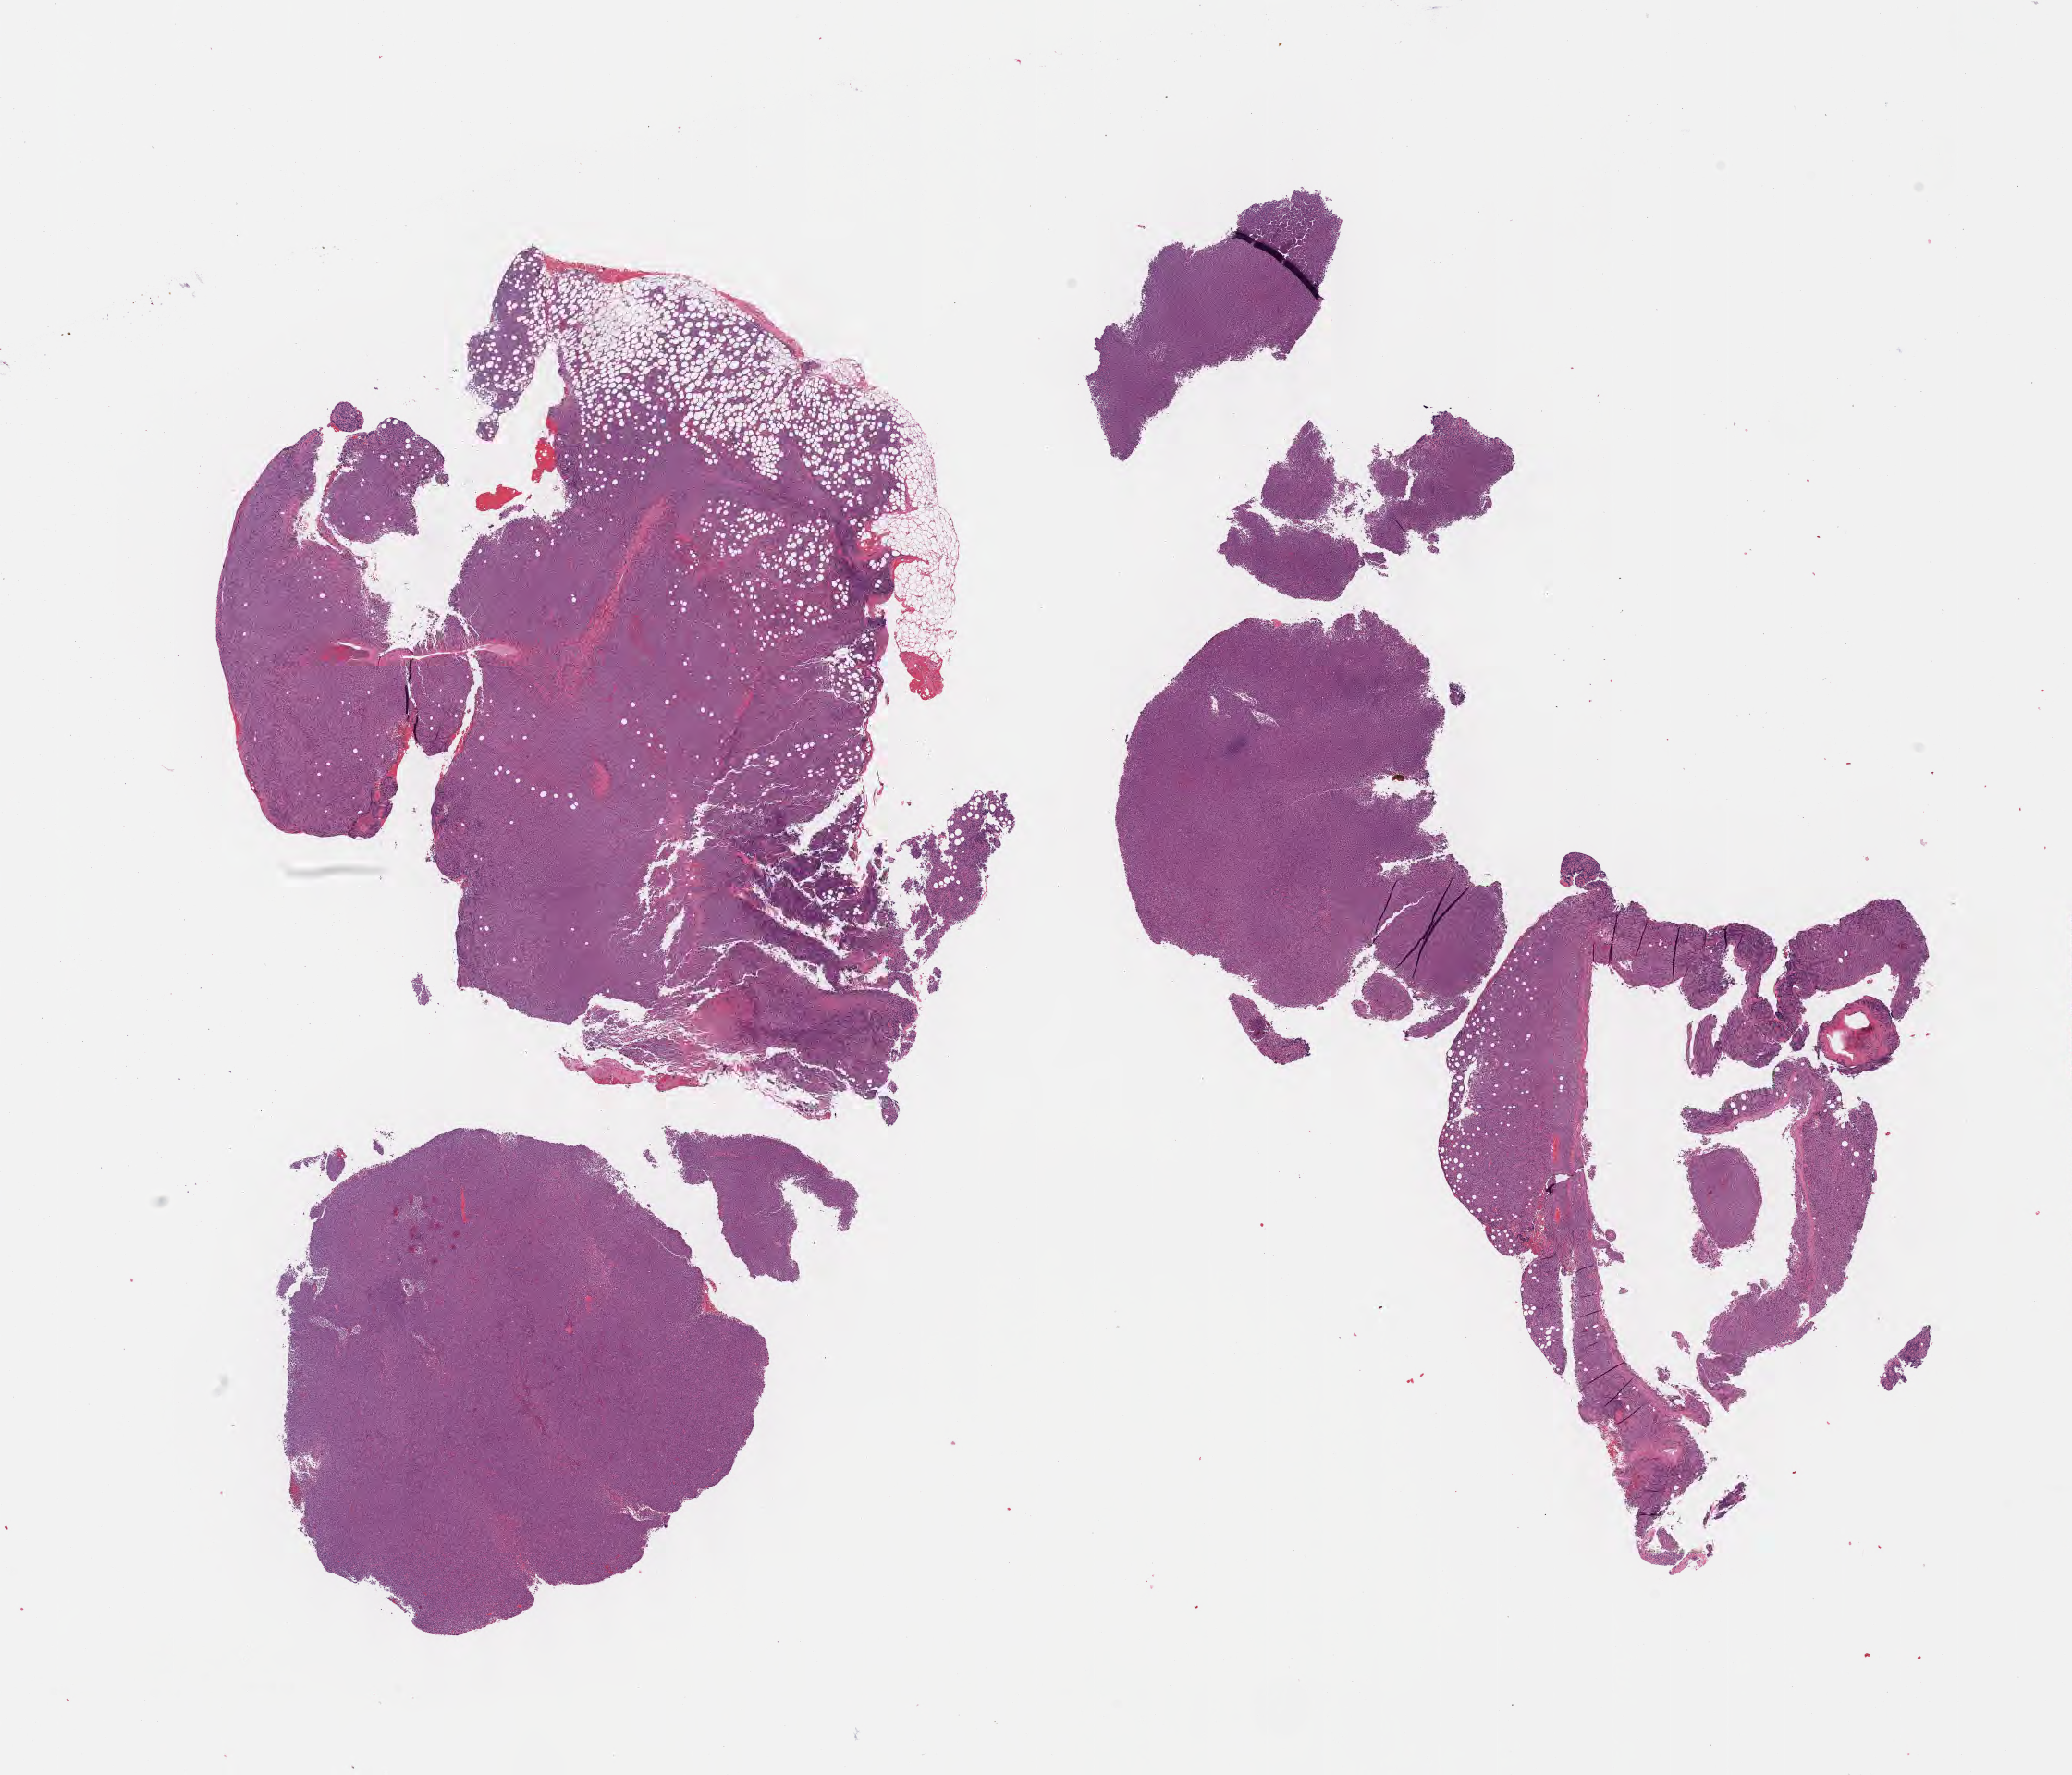
H&E whole-slide image — low-resolution overview of the scanned area, about 18.1 x 15.5 mm. Specimen: tumor tissue. Female patient, age 32 years.
Histologic diagnosis: Diffuse large B-cell lymphoma, NOS.